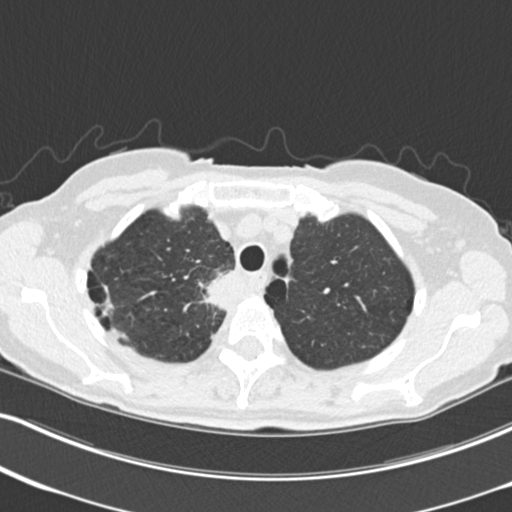
Axial slice from a low-dose chest CT screening exam. Third screening round (two years after baseline). Lung window (W 1500 / L -600 HU). 2 mm slice thickness. Standard (soft-tissue) reconstruction kernel (B30f). 512 × 512 image matrix, field of view 322 × 322 mm. Female participant, aged 68 years at enrolment. Current smoker at enrolment.
Expert reader's lesion annotation, bounding box <200,264,251,319> (left, top, right, bottom; pixels). The exam's reader record, not a measurement of the box and not confirmed to be the same lesion: non-calcified nodule or mass ≥4 mm, right upper lobe, 31 × 29 mm, poorly defined margins, soft tissue attenuation, pre-existing on the prior screen: no. Participant outcome: lung cancer diagnosed 79 days after this screen — squamous cell carcinoma, NOS, right upper lobe, mediastinum, poorly differentiated (G3), stage IIIB (AJCC 6th edition), 43 mm at pathology.